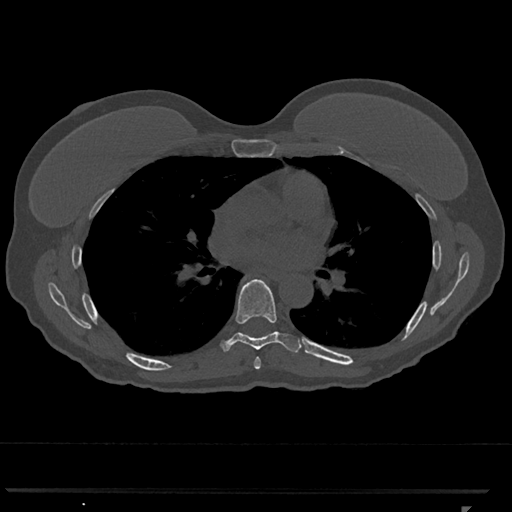
CT including the spine, one axial slice. Position 713 of 793 along the scan axis. Bone window (W 1800 / L 400 HU). 0.5 mm slice thickness. 512 × 512 image matrix, field of view 380 × 380 mm. Female patient, age 62 years. From the clinical record (not read from this slice): primary cancer: renal.
Structures marked on this image (semi-automatically segmented with operator editing):
- T6 vertebra: bounding box [x1, y1, x2, y2] px = [254, 357, 261, 370]
- T7 vertebra: [220, 279, 302, 352]